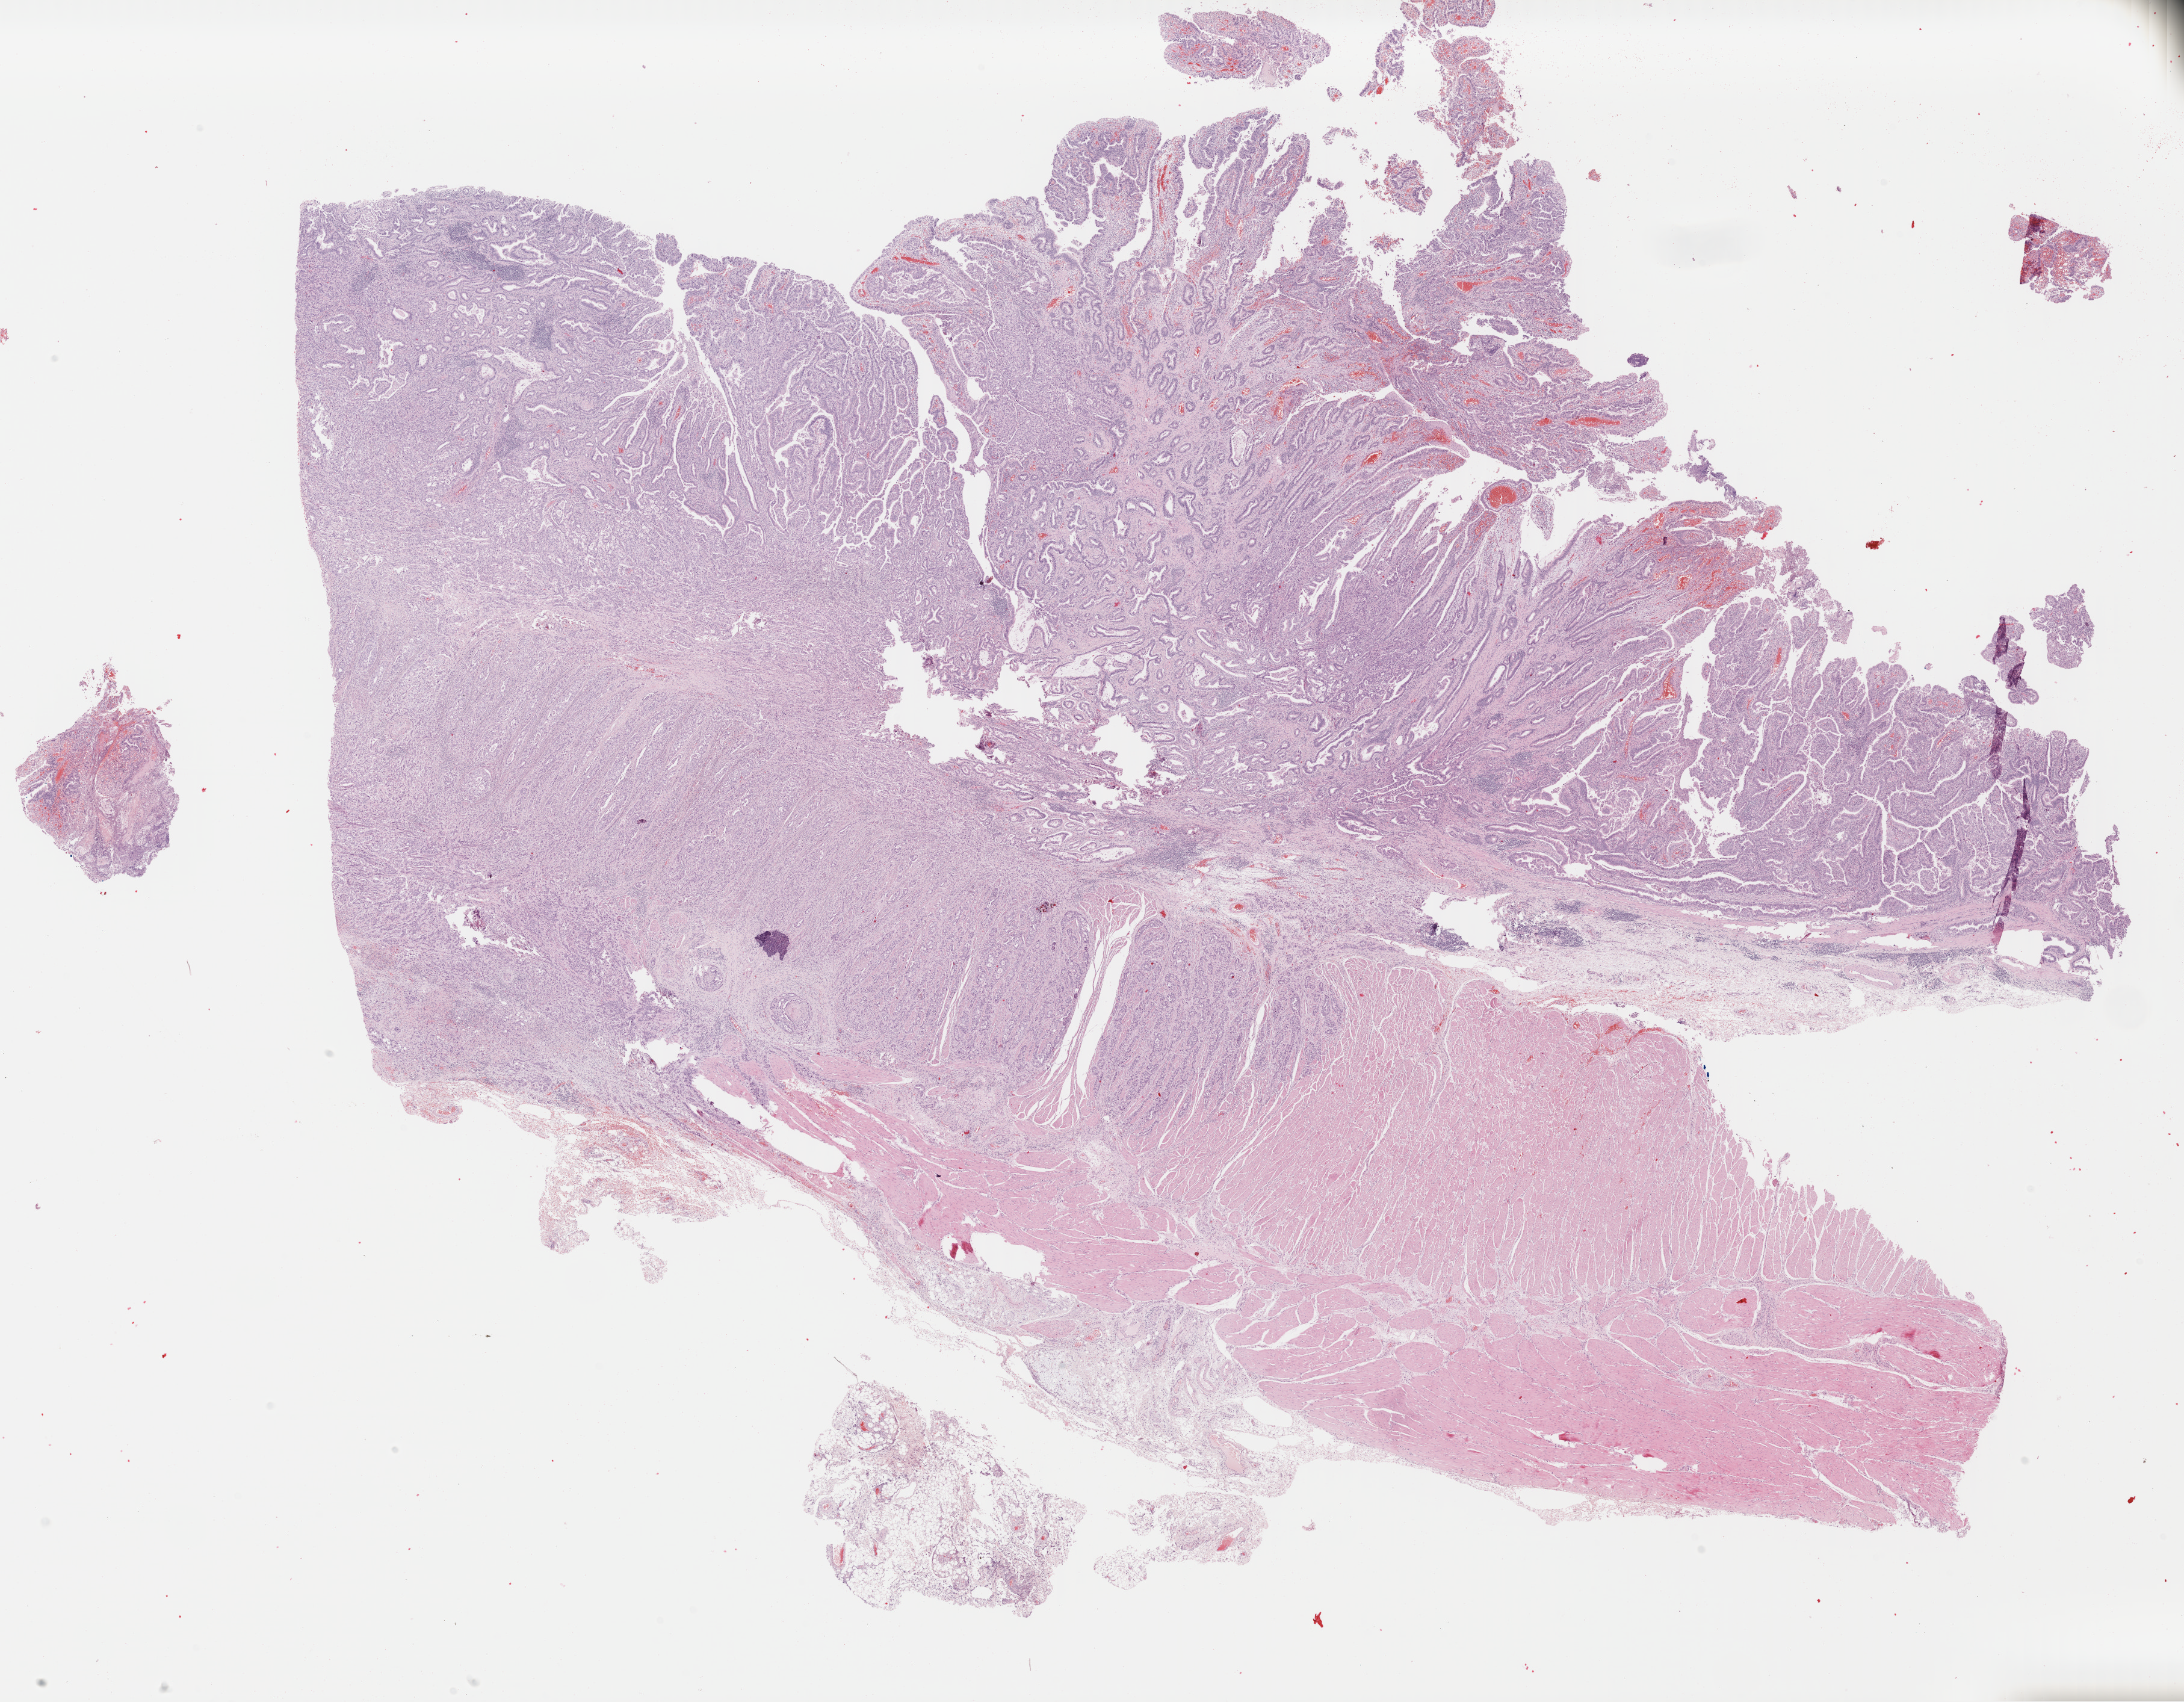
H&E-stained whole-slide image, low-resolution overview of the scanned area, about 28.5 x 22.2 mm (from a 40x scan), formalin-fixed paraffin-embedded (FFPE) diagnostic section, sample: primary tumour, stomach. Male patient; age at initial diagnosis 58 years. Histologic grade: G3 (poorly differentiated).
Lymph nodes positive (case pathology): 6 of 9 examined. TNM: T2 N2 M0. AJCC pathologic stage: IIIA (6th edition). Pathologic diagnosis: Carcinoma, diffuse type (cardia, NOS).